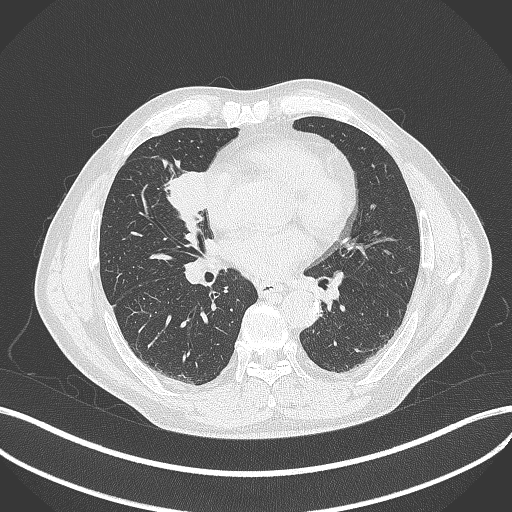
Chest CT, one axial slice; position 189 of 429 along the scan axis; 120 kVp; lung window (W 1500 / L -600 HU); 1 mm slice thickness; 512 × 512 image matrix, field of view 400 × 400 mm. Male patient, age 61 years. Case-level facts recorded for this patient, not image findings: clinical TNM (as recorded): T2b N1 M0.
Outlined on this slice (rectangle marked by the reading radiologist):
- lung tumour (recorded histology: squamous cell carcinoma): bounding box [x1, y1, x2, y2] px = [156, 163, 212, 223]